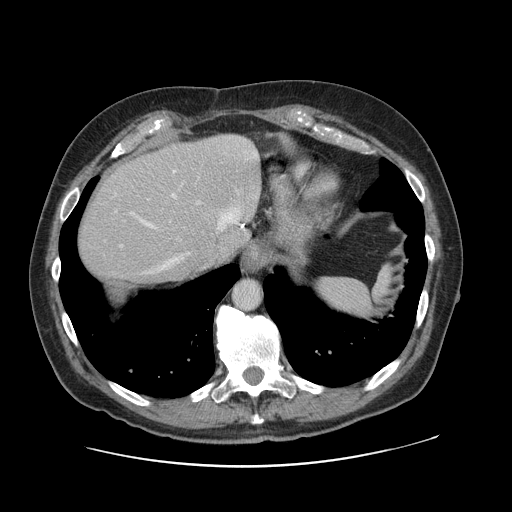
Contrast-enhanced abdominal CT, one axial slice; slice 97 of 138 in the series (ordered by position); 120 kVp; intravenous contrast given; soft-tissue window (W 400 / L 40 HU); 2.5 mm slice thickness; 512 × 512 image matrix, field of view 402 × 402 mm. Male patient, age 71 years. From the clinical record (not read from this slice): diagnosis: colorectal cancer liver metastases, imaged before liver resection; multiple liver metastases: no; largest metastasis: 3.3 cm.
Outlined on this slice (outlined manually by an expert reader):
- hepatic veins: box from (x=143, y=207) to (x=244, y=269) px
- liver: (x=77, y=135)–(x=261, y=287)
- planned liver remnant (the part of the liver to remain after resection): (x=77, y=159)–(x=223, y=287)